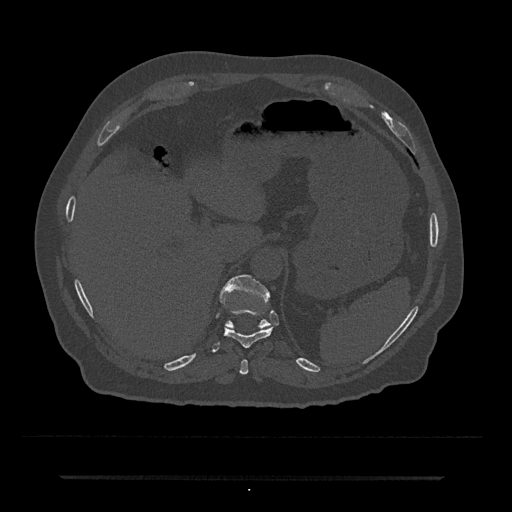
CT including the spine, one axial slice; slice 219 of 797 in the series (ordered by position); reconstruction kernel Br40s/3; 120 kVp; bone window (W 1800 / L 400 HU); 0.5 mm slice thickness; 512 × 512 image matrix, field of view 437 × 437 mm. Patient: male, 69 years. From the clinical record (not read from this slice): primary cancer: prostate.
Outlined on this slice (semi-automatic segmentation, software-assisted and operator-edited):
- T10 vertebra: bounding box (x1, y1, x2, y2) in pixels: (212, 309, 273, 353)
- T11 vertebra: (219, 275, 271, 329)
- T9 vertebra: (239, 359, 248, 375)